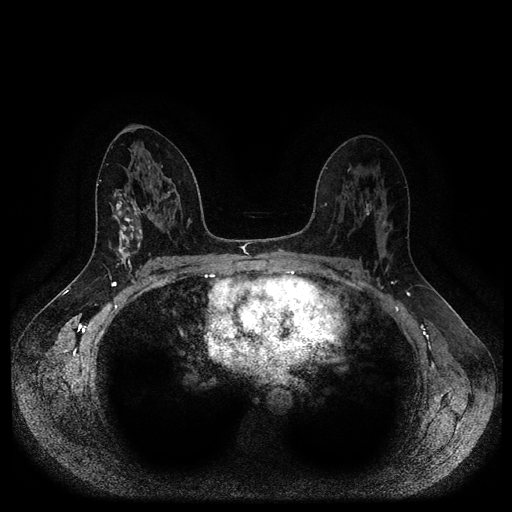
Breast MRI (dynamic contrast-enhanced, multi-phase), one axial slice. Slice 58 of 116 in the series (ordered by position). Dynamic contrast-enhanced series, time point 2 of 5 at this slice position (early post-contrast). 1.5 T. TE 2.6 ms, TR 5.3 ms. 512 × 512 image matrix, field of view 360 × 360 mm. Female patient, age 45 years.
Structures marked on this image (semi-automatically segmented with operator editing):
- breast lesion (labelled benign in the annotation): box from (x=108, y=189) to (x=143, y=277) px